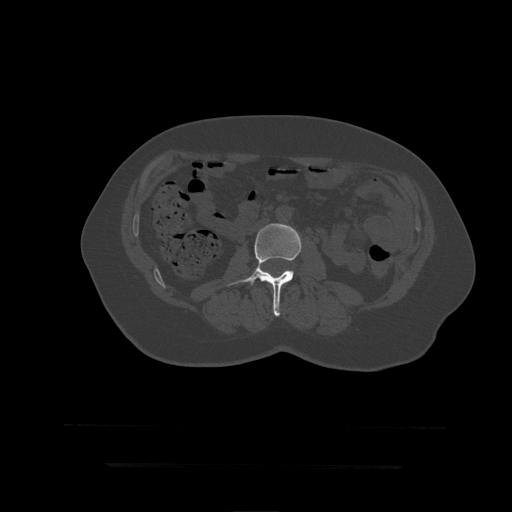
CT including the spine, one axial slice; position 122 of 399 along the scan axis; reconstruction kernel STANDARD; bone window (W 1800 / L 400 HU); 1.25 mm slice thickness; 512 × 512 image matrix. Patient age 41 years. From the clinical record (not read from this slice): primary cancer: breast.
Structures marked on this image (semi-automatically segmented with operator editing):
- L3 vertebra: bounding box <227,224,302,317> (left, top, right, bottom; pixels)